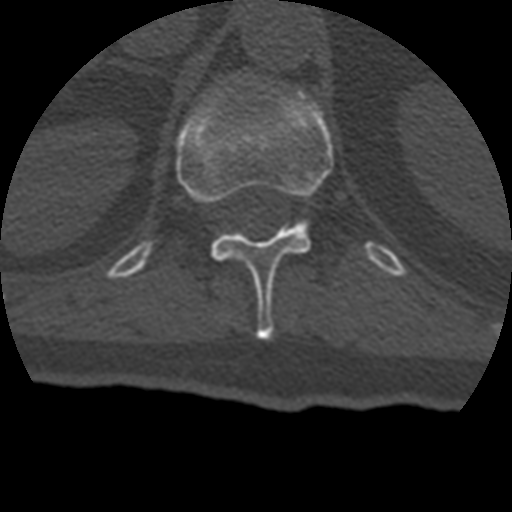
CT including the spine, one axial slice. Slice 167 of 399 in the series (ordered by position). Reconstruction kernel STANDARD. 120 kVp. Bone window (W 1800 / L 400 HU). 1.25 mm slice thickness. 512 × 512 image matrix, field of view 160 × 160 mm. Patient age 69 years. From the clinical record (not read from this slice): primary cancer: prostate.
Structures marked on this image (semi-automatic segmentation, software-assisted and operator-edited):
- T12 vertebra: bounding box (x1, y1, x2, y2) in pixels: (176, 89, 334, 340)